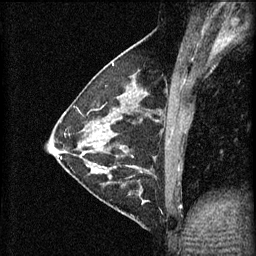
Breast MRI (dynamic contrast-enhanced), one sagittal slice; position 24 of 60 along the scan axis; 3 images stored at this slice position (order not interpretable as contrast timing); 1.5 T; TE 4.2 ms, TR 11 ms; 2 mm slice thickness; 256 × 256 image matrix, field of view 180 × 180 mm. Female patient, age 29 years.
Structures marked on this image (semi-automatic segmentation, software-assisted and operator-edited):
- analysis volume of interest (the breast-tissue region the enhancement analysis was run in; not a lesion): bounding box [x1, y1, x2, y2] px = [105, 172, 171, 227]
- tumour enhancement mask (voxels above the 70 % enhancement threshold inside the analysis volume of interest): [106, 172, 149, 205]